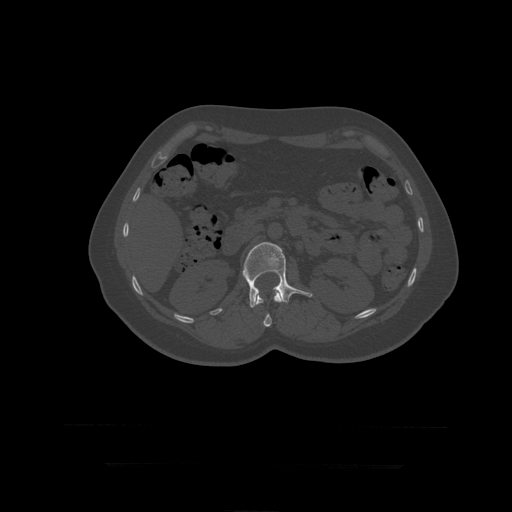
CT including the spine, one axial slice; slice 157 of 399 in the series (ordered by position); bone window (W 1800 / L 400 HU); 1.25 mm slice thickness; 512 × 512 image matrix, field of view 450 × 450 mm. Patient age 41 years. Case-level facts recorded for this patient, not image findings: primary cancer: breast.
Outlined on this slice (semi-automatic segmentation, software-assisted and operator-edited):
- L1 vertebra: bounding box (x1, y1, x2, y2) in pixels: (256, 289, 283, 327)
- L2 vertebra: (243, 243, 313, 308)